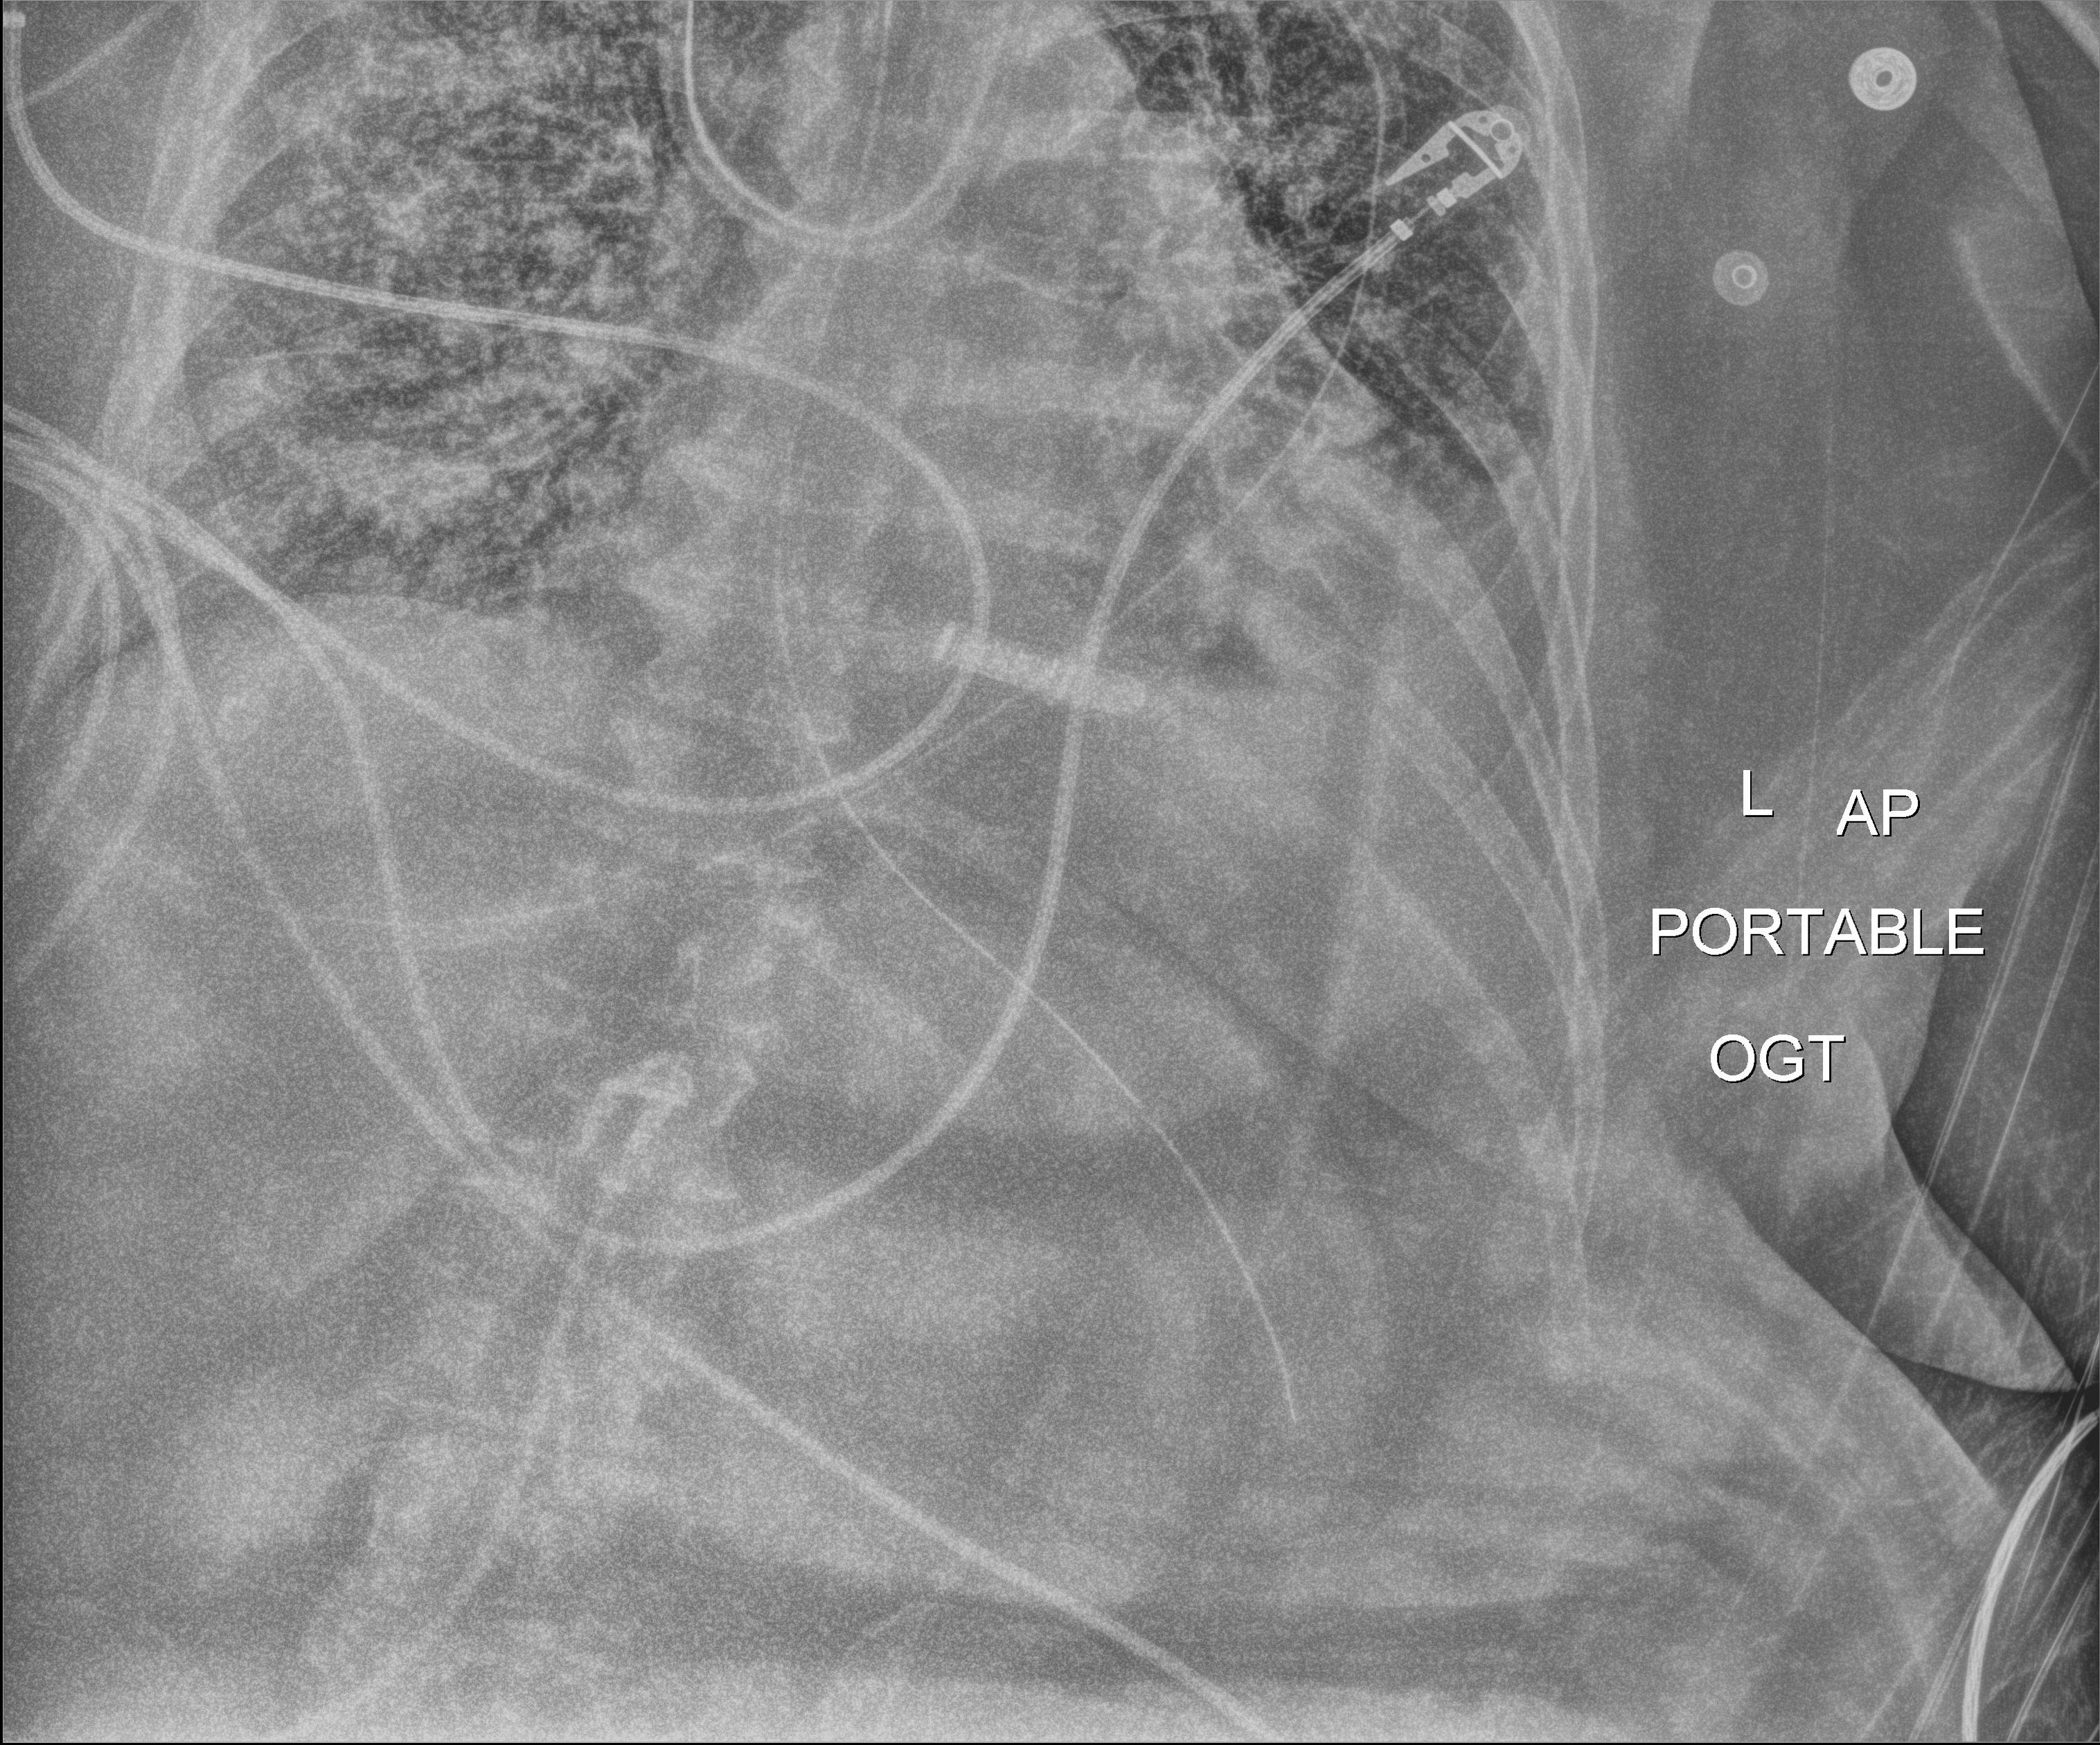
Bedside chest radiograph (digital radiography); anteroposterior (AP) projection. Patient hospitalised with COVID-19; female, aged 60–74 years.
Hospital-stay facts (about this admission, not read from this image; timing relative to this image not recorded):
- admitted to intensive care during this hospital stay: yes
- other chronic lung disease (admission record): yes